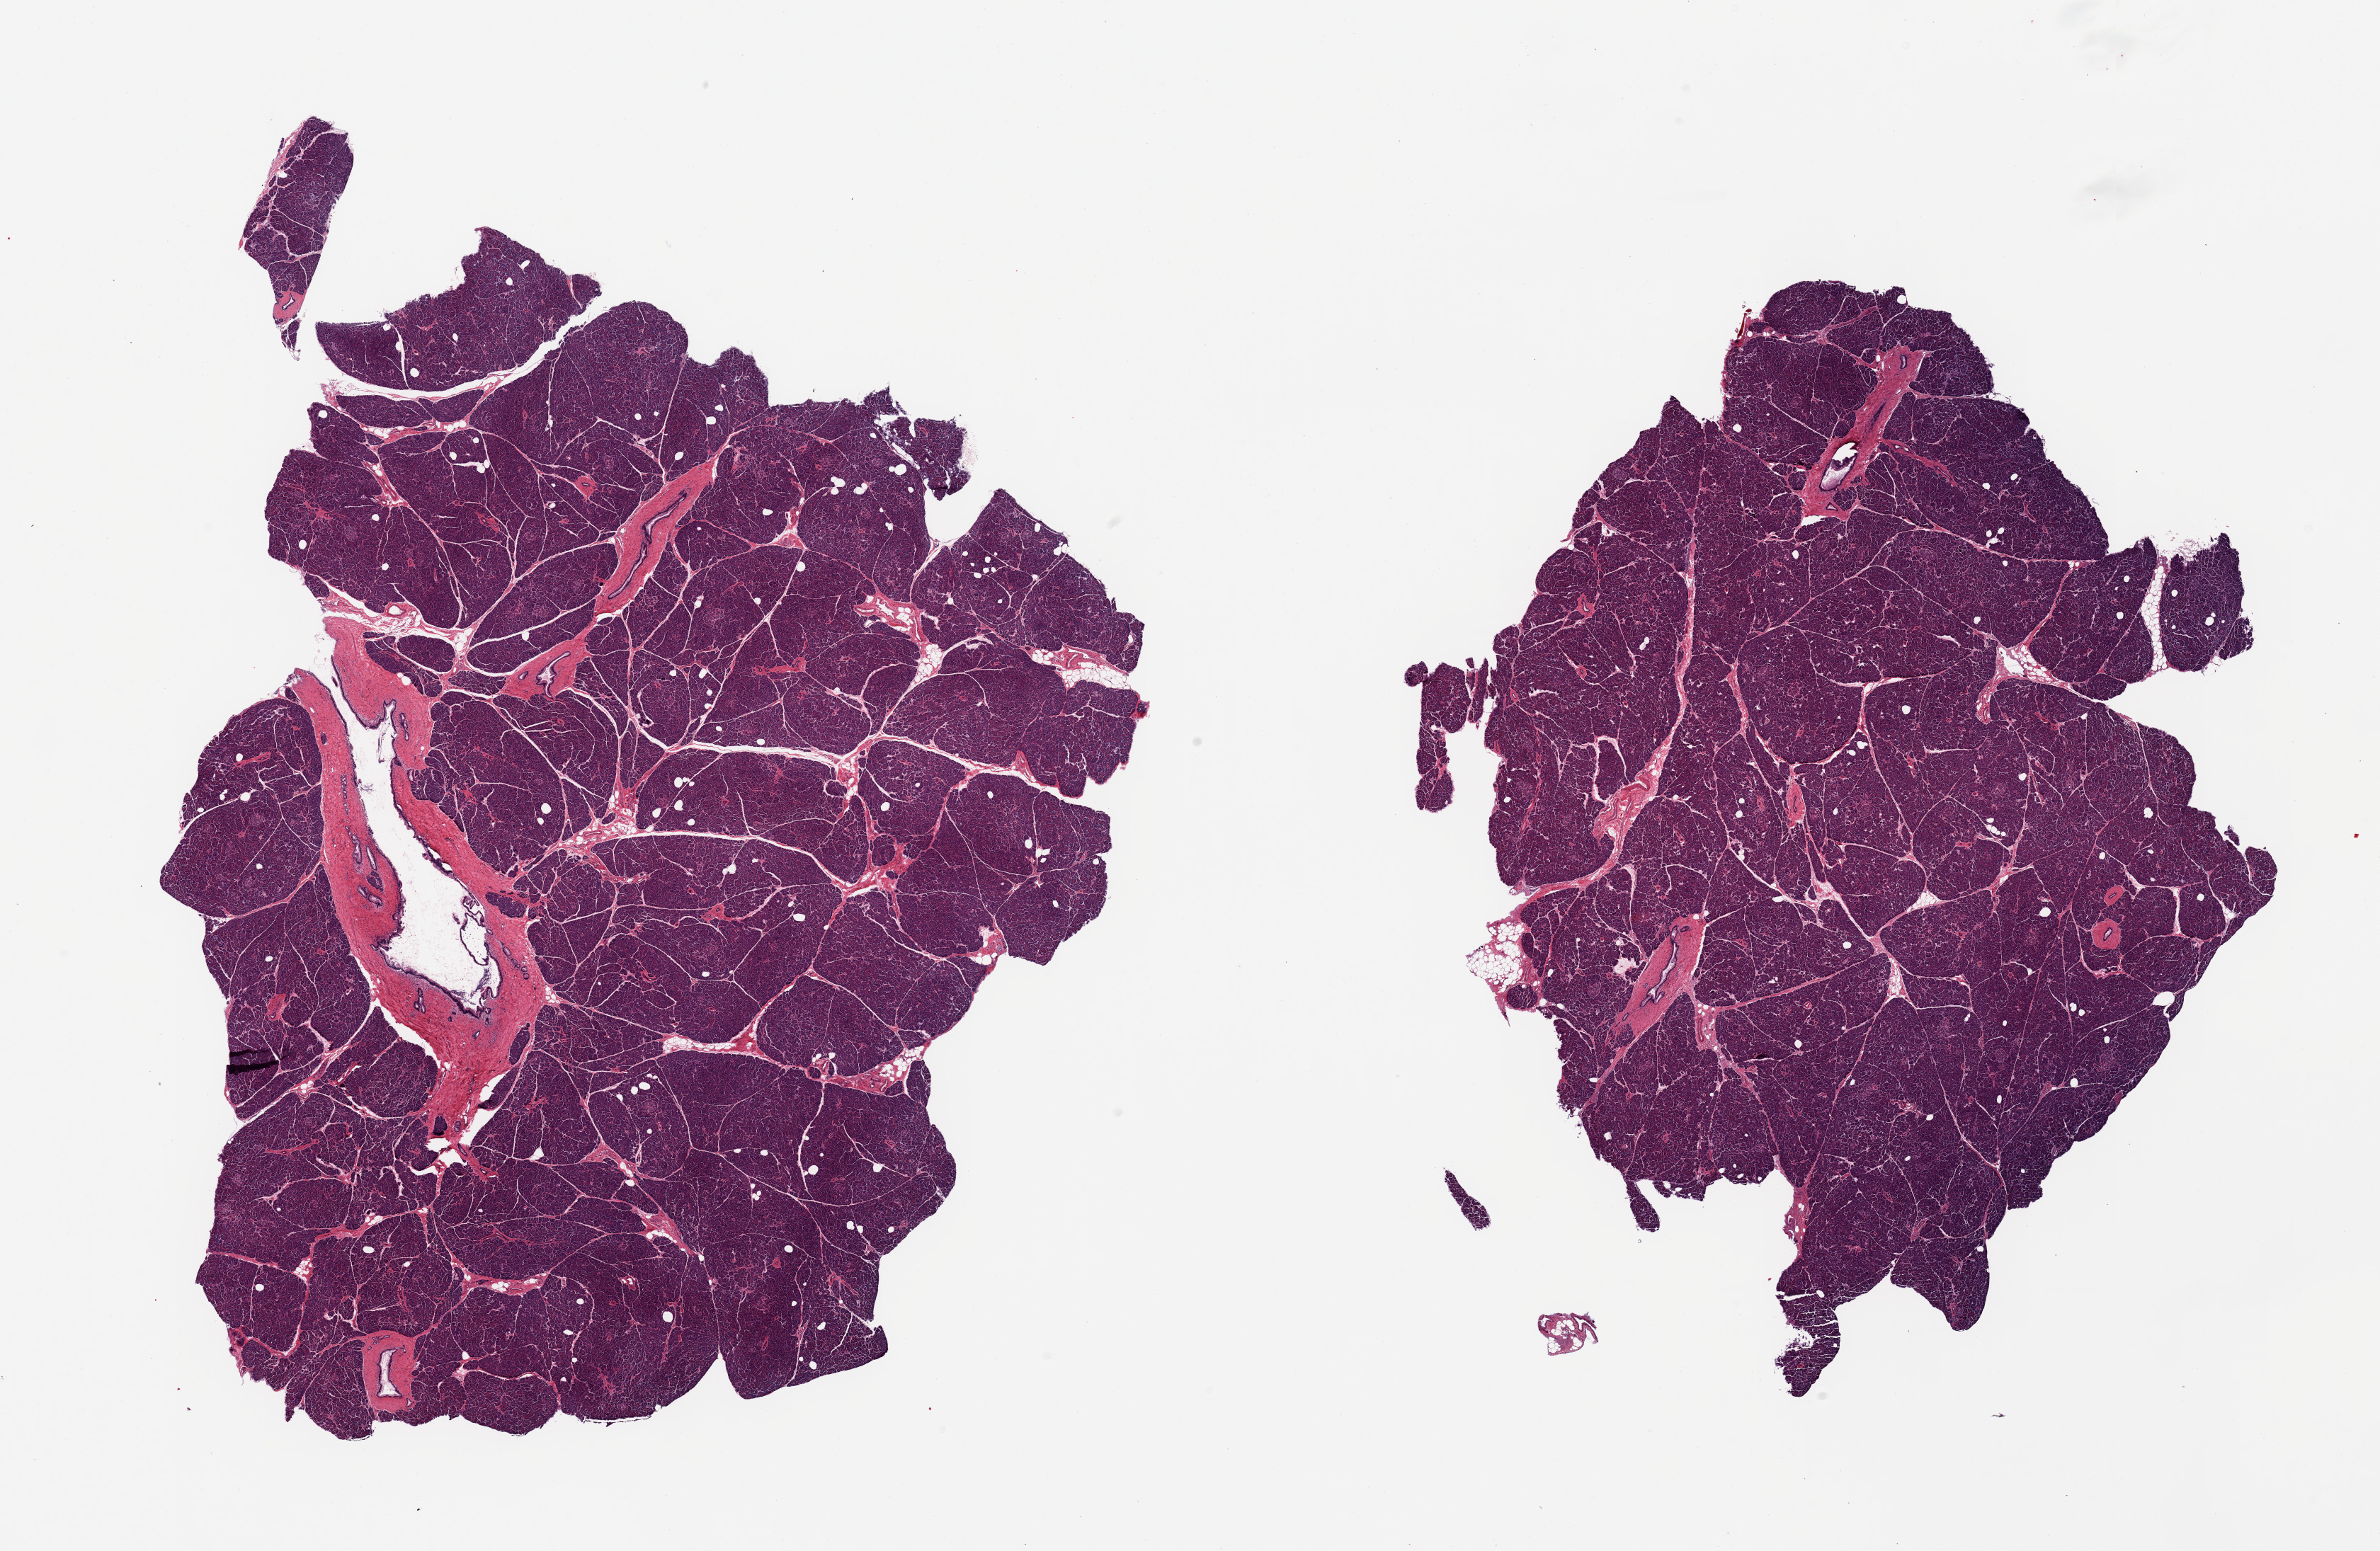
Whole-slide image, hematoxylin and eosin (H&E) stain, brightfield, low-resolution overview of the scanned area, about 26.6 x 17.3 mm. PAXgene-fixed paraffin-embedded (PFPE) section. Target tissue: pancreas. Tissue donor sample. Donor: female.
Reviewer comment on this tissue sample: 2 pieces, well preserved, Islets well visualized; Minimal fat; good specimen.